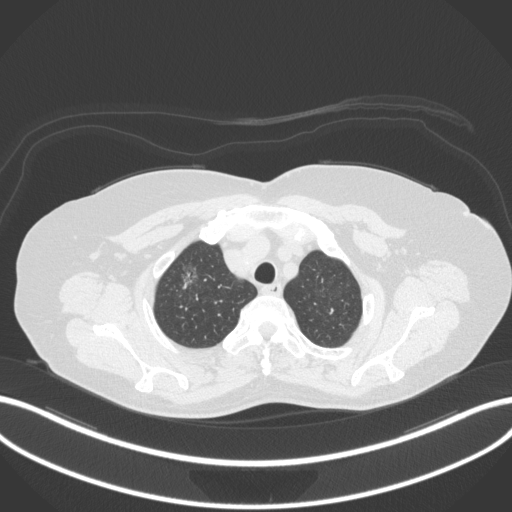
Chest CT, one axial slice; slice 300 of 365 in the series (ordered by position); reconstruction kernel B31f; lung window (W 1500 / L -600 HU); 1 mm slice thickness; 512 × 512 image matrix, field of view 400 × 400 mm. Female patient, age 62 years. Case-level facts recorded for this patient, not image findings: clinical TNM (as recorded): T1c N0 M0.
Annotated regions visible in this slice (rectangle marked by the reading radiologist):
- lung tumour (recorded histology: adenocarcinoma): box from (x=176, y=259) to (x=208, y=297) px